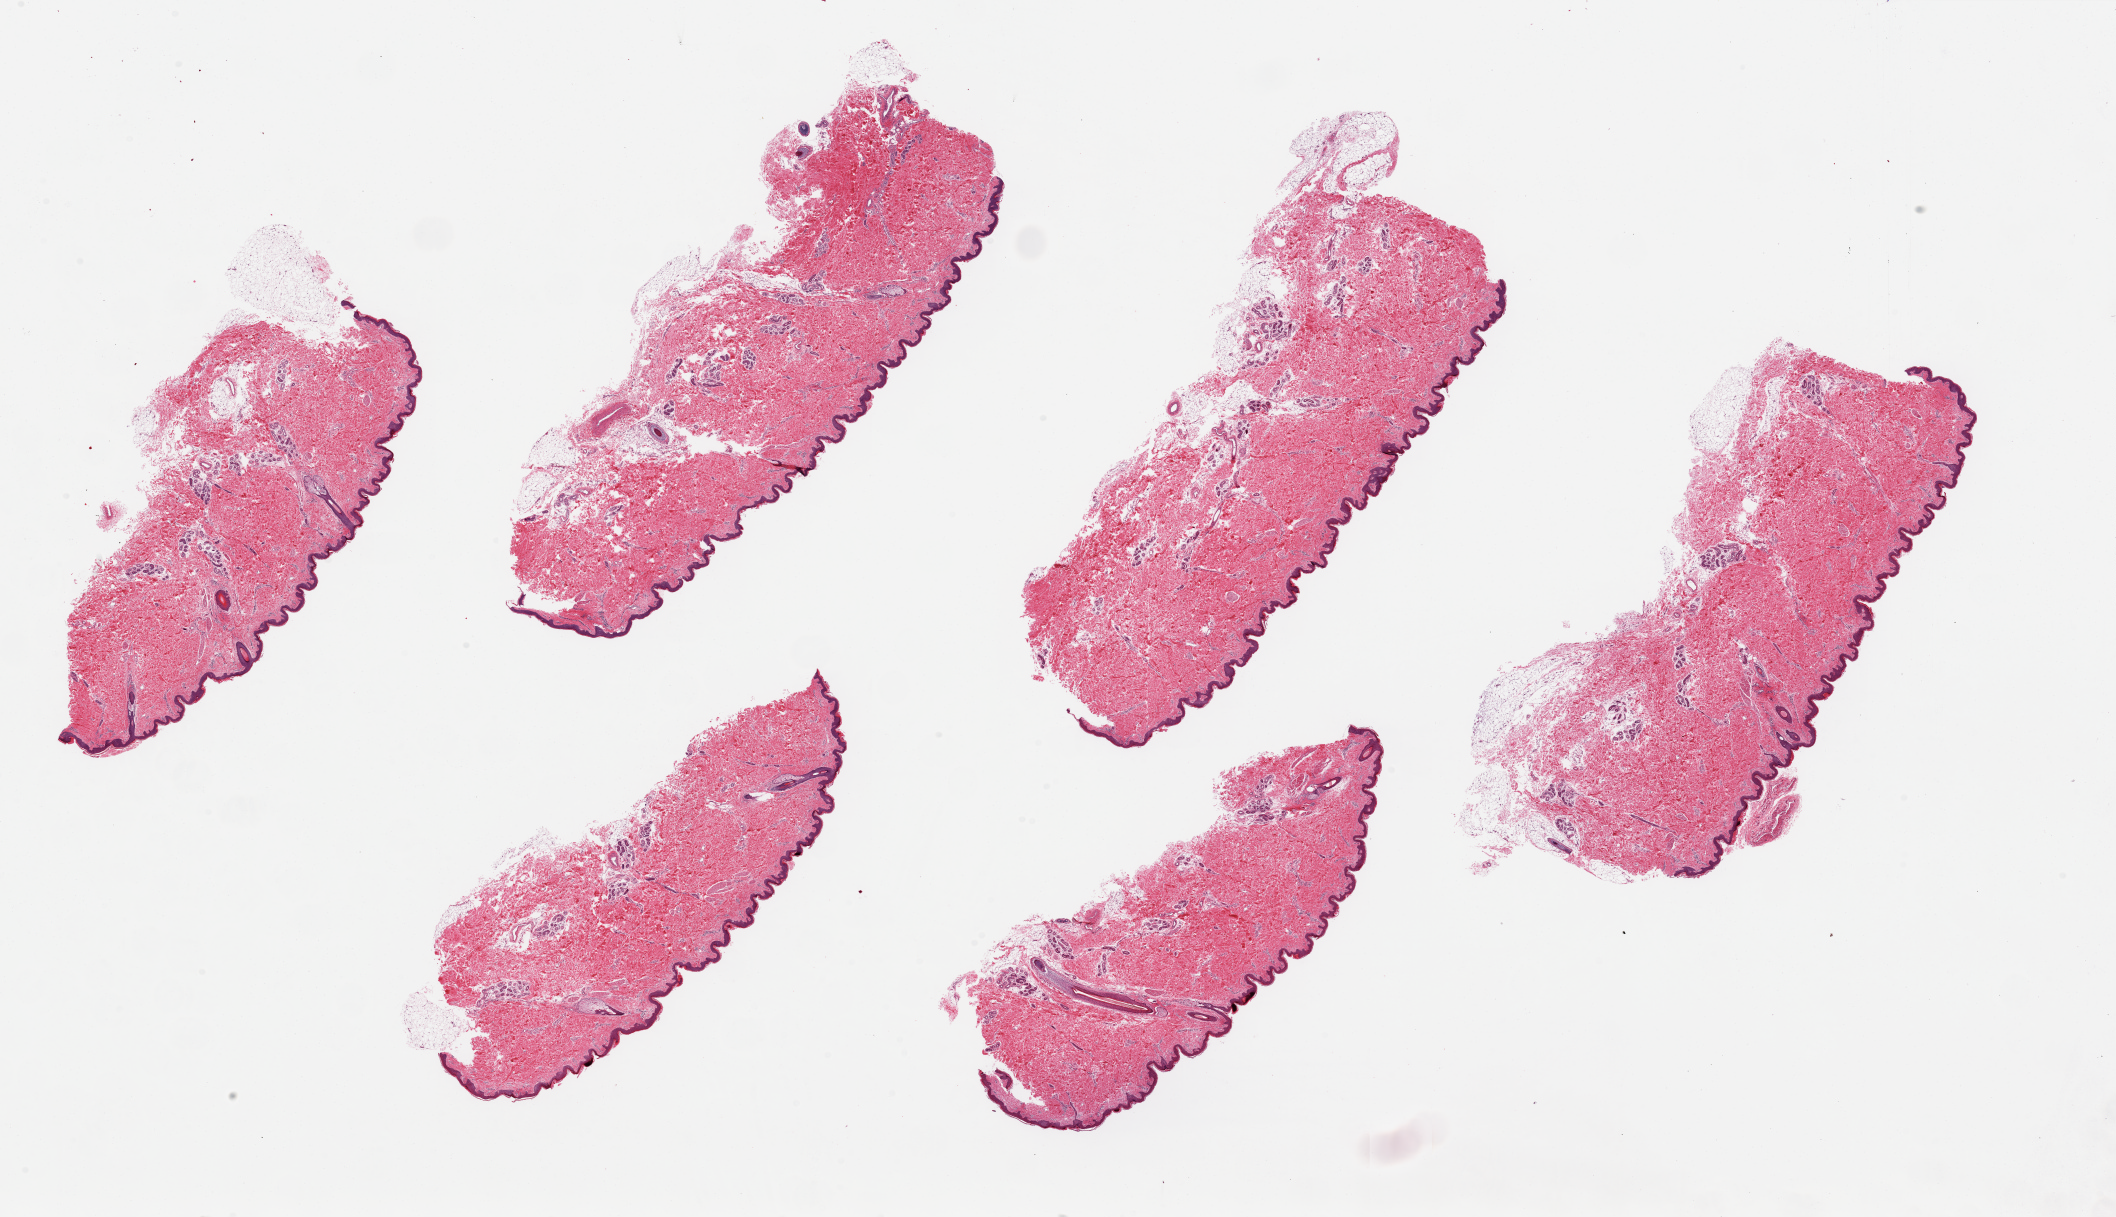
Whole-slide image, haematoxylin and eosin stain, brightfield — shown as a low-resolution overview of the whole scanned area (about 33.5 x 19.3 mm), PAXgene-fixed paraffin-embedded (PFPE) section, sampled site (target tissue): skin of lower leg, tissue donor sample. Donor sex: male.
• reviewer comment on this tissue sample: 6 pieces, ~9x4mm. Squamous epithelium is ~2-3% of thickness